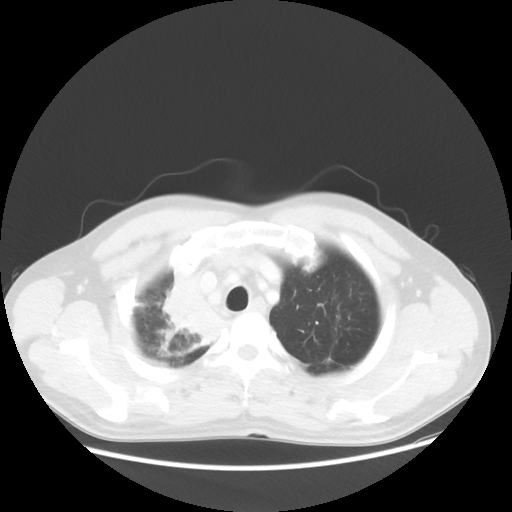
Chest CT, one axial slice. 100 kVp. Lung window (W 1500 / L -600 HU). 512 × 512 image matrix, field of view 398 × 398 mm. Male patient, age 60 years. Case-level facts recorded for this patient, not image findings: clinical TNM (as recorded): T2a N1 M0.
Outlined on this slice (rectangle marked by the reading radiologist):
- lung tumour (recorded histology: squamous cell carcinoma): box from (x=142, y=254) to (x=231, y=363) px